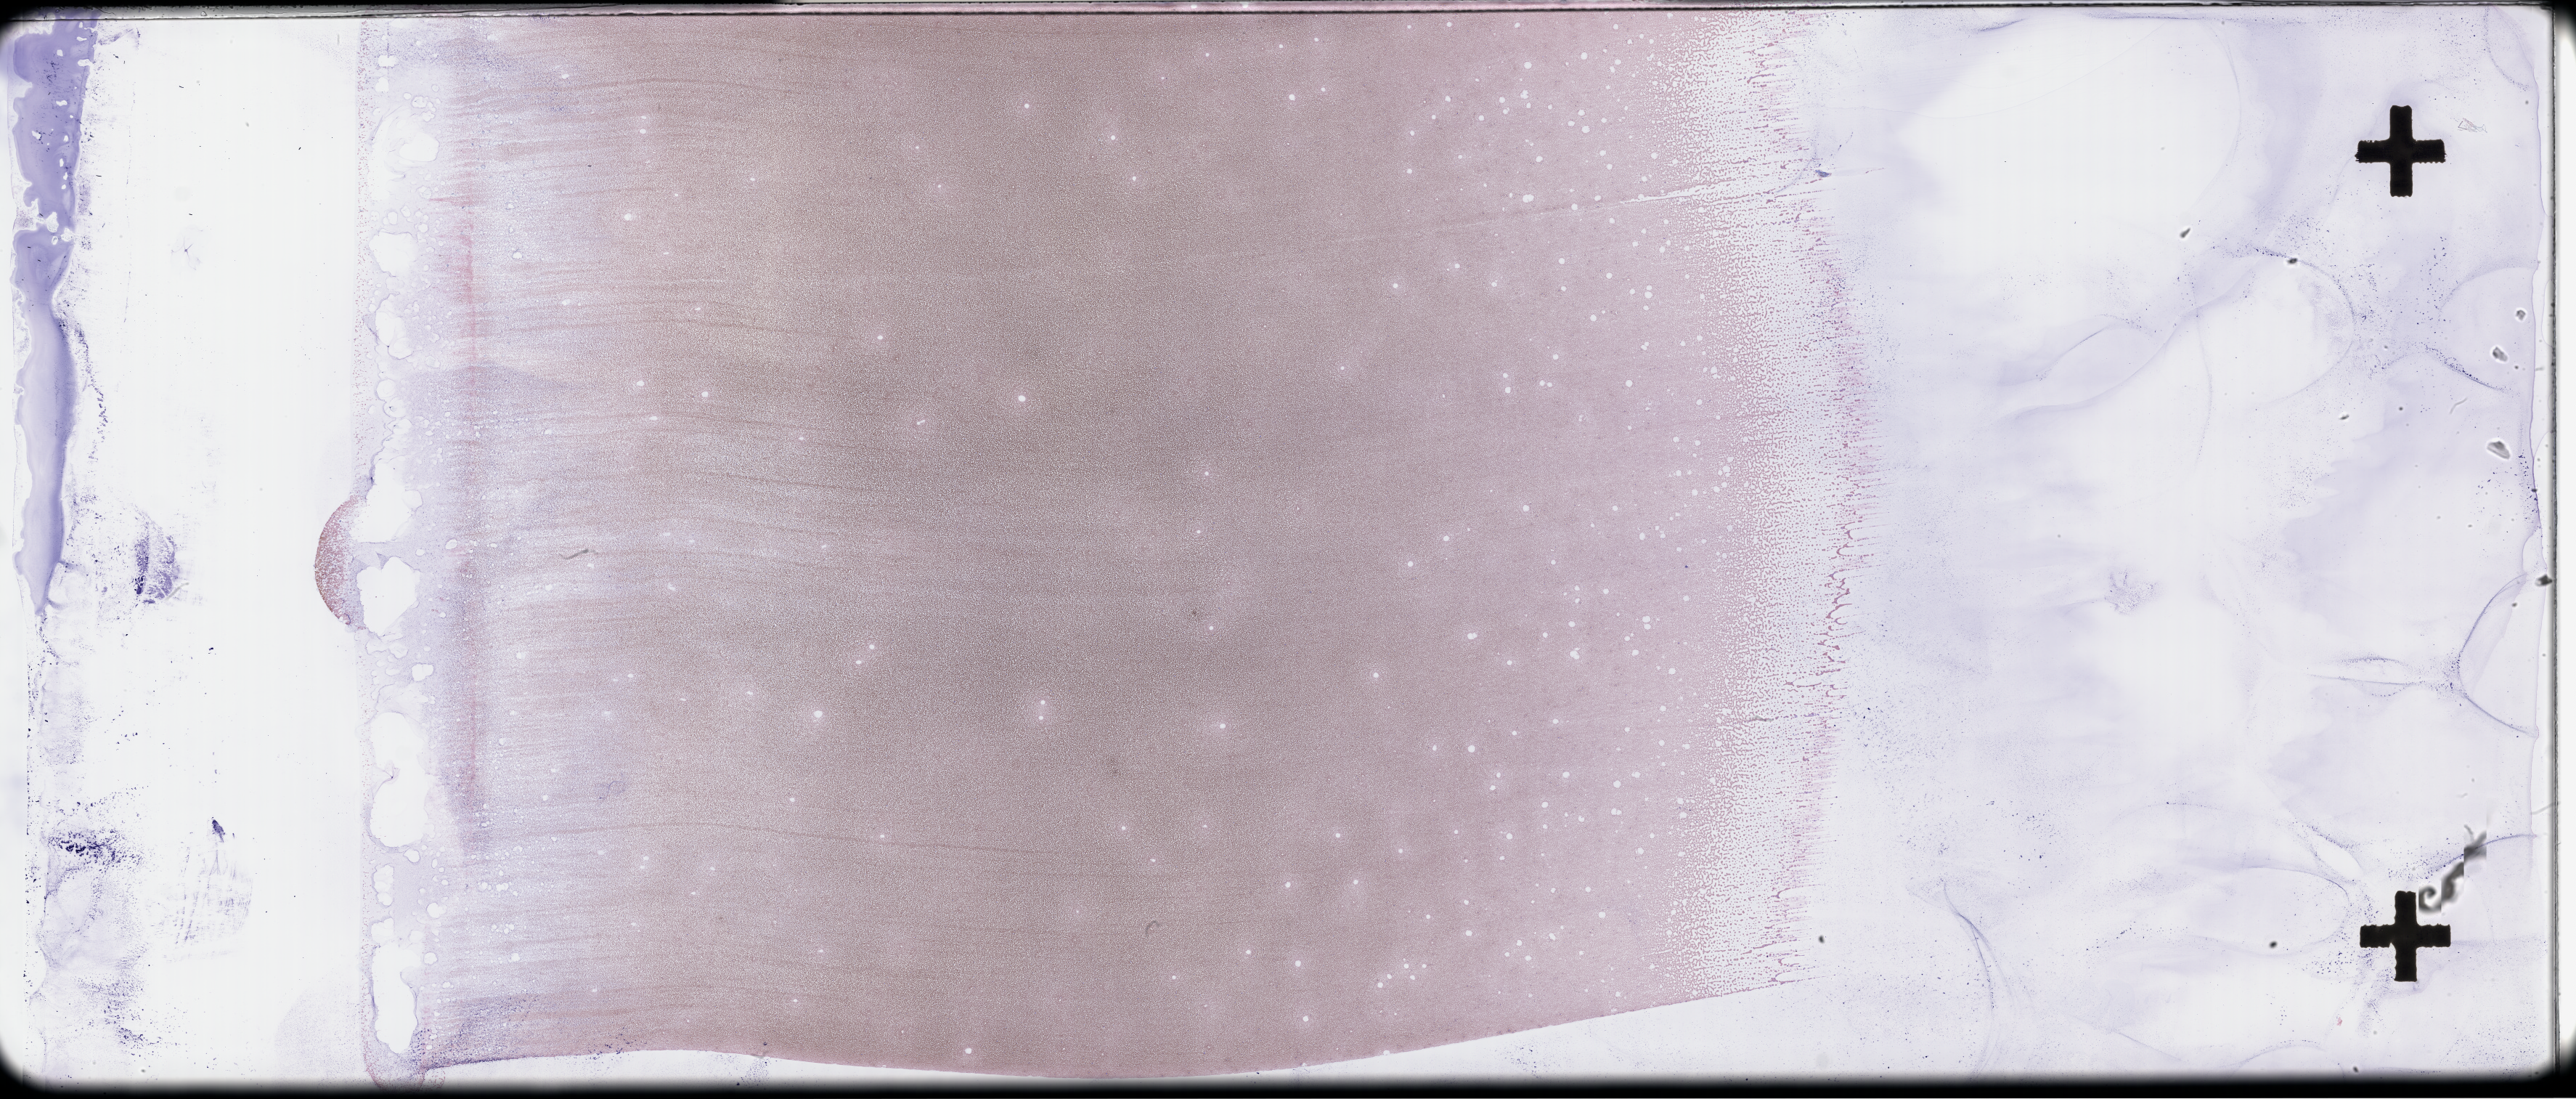
Wright–Giemsa-stained whole blood smear, whole-slide image — whole scanned area (about 57.3 x 24.4 mm) shown as a low-resolution overview; collected post-treatment, no progression. Patient: female.
From a patient with: Acute Myeloid Leukemia Not Otherwise Specified.